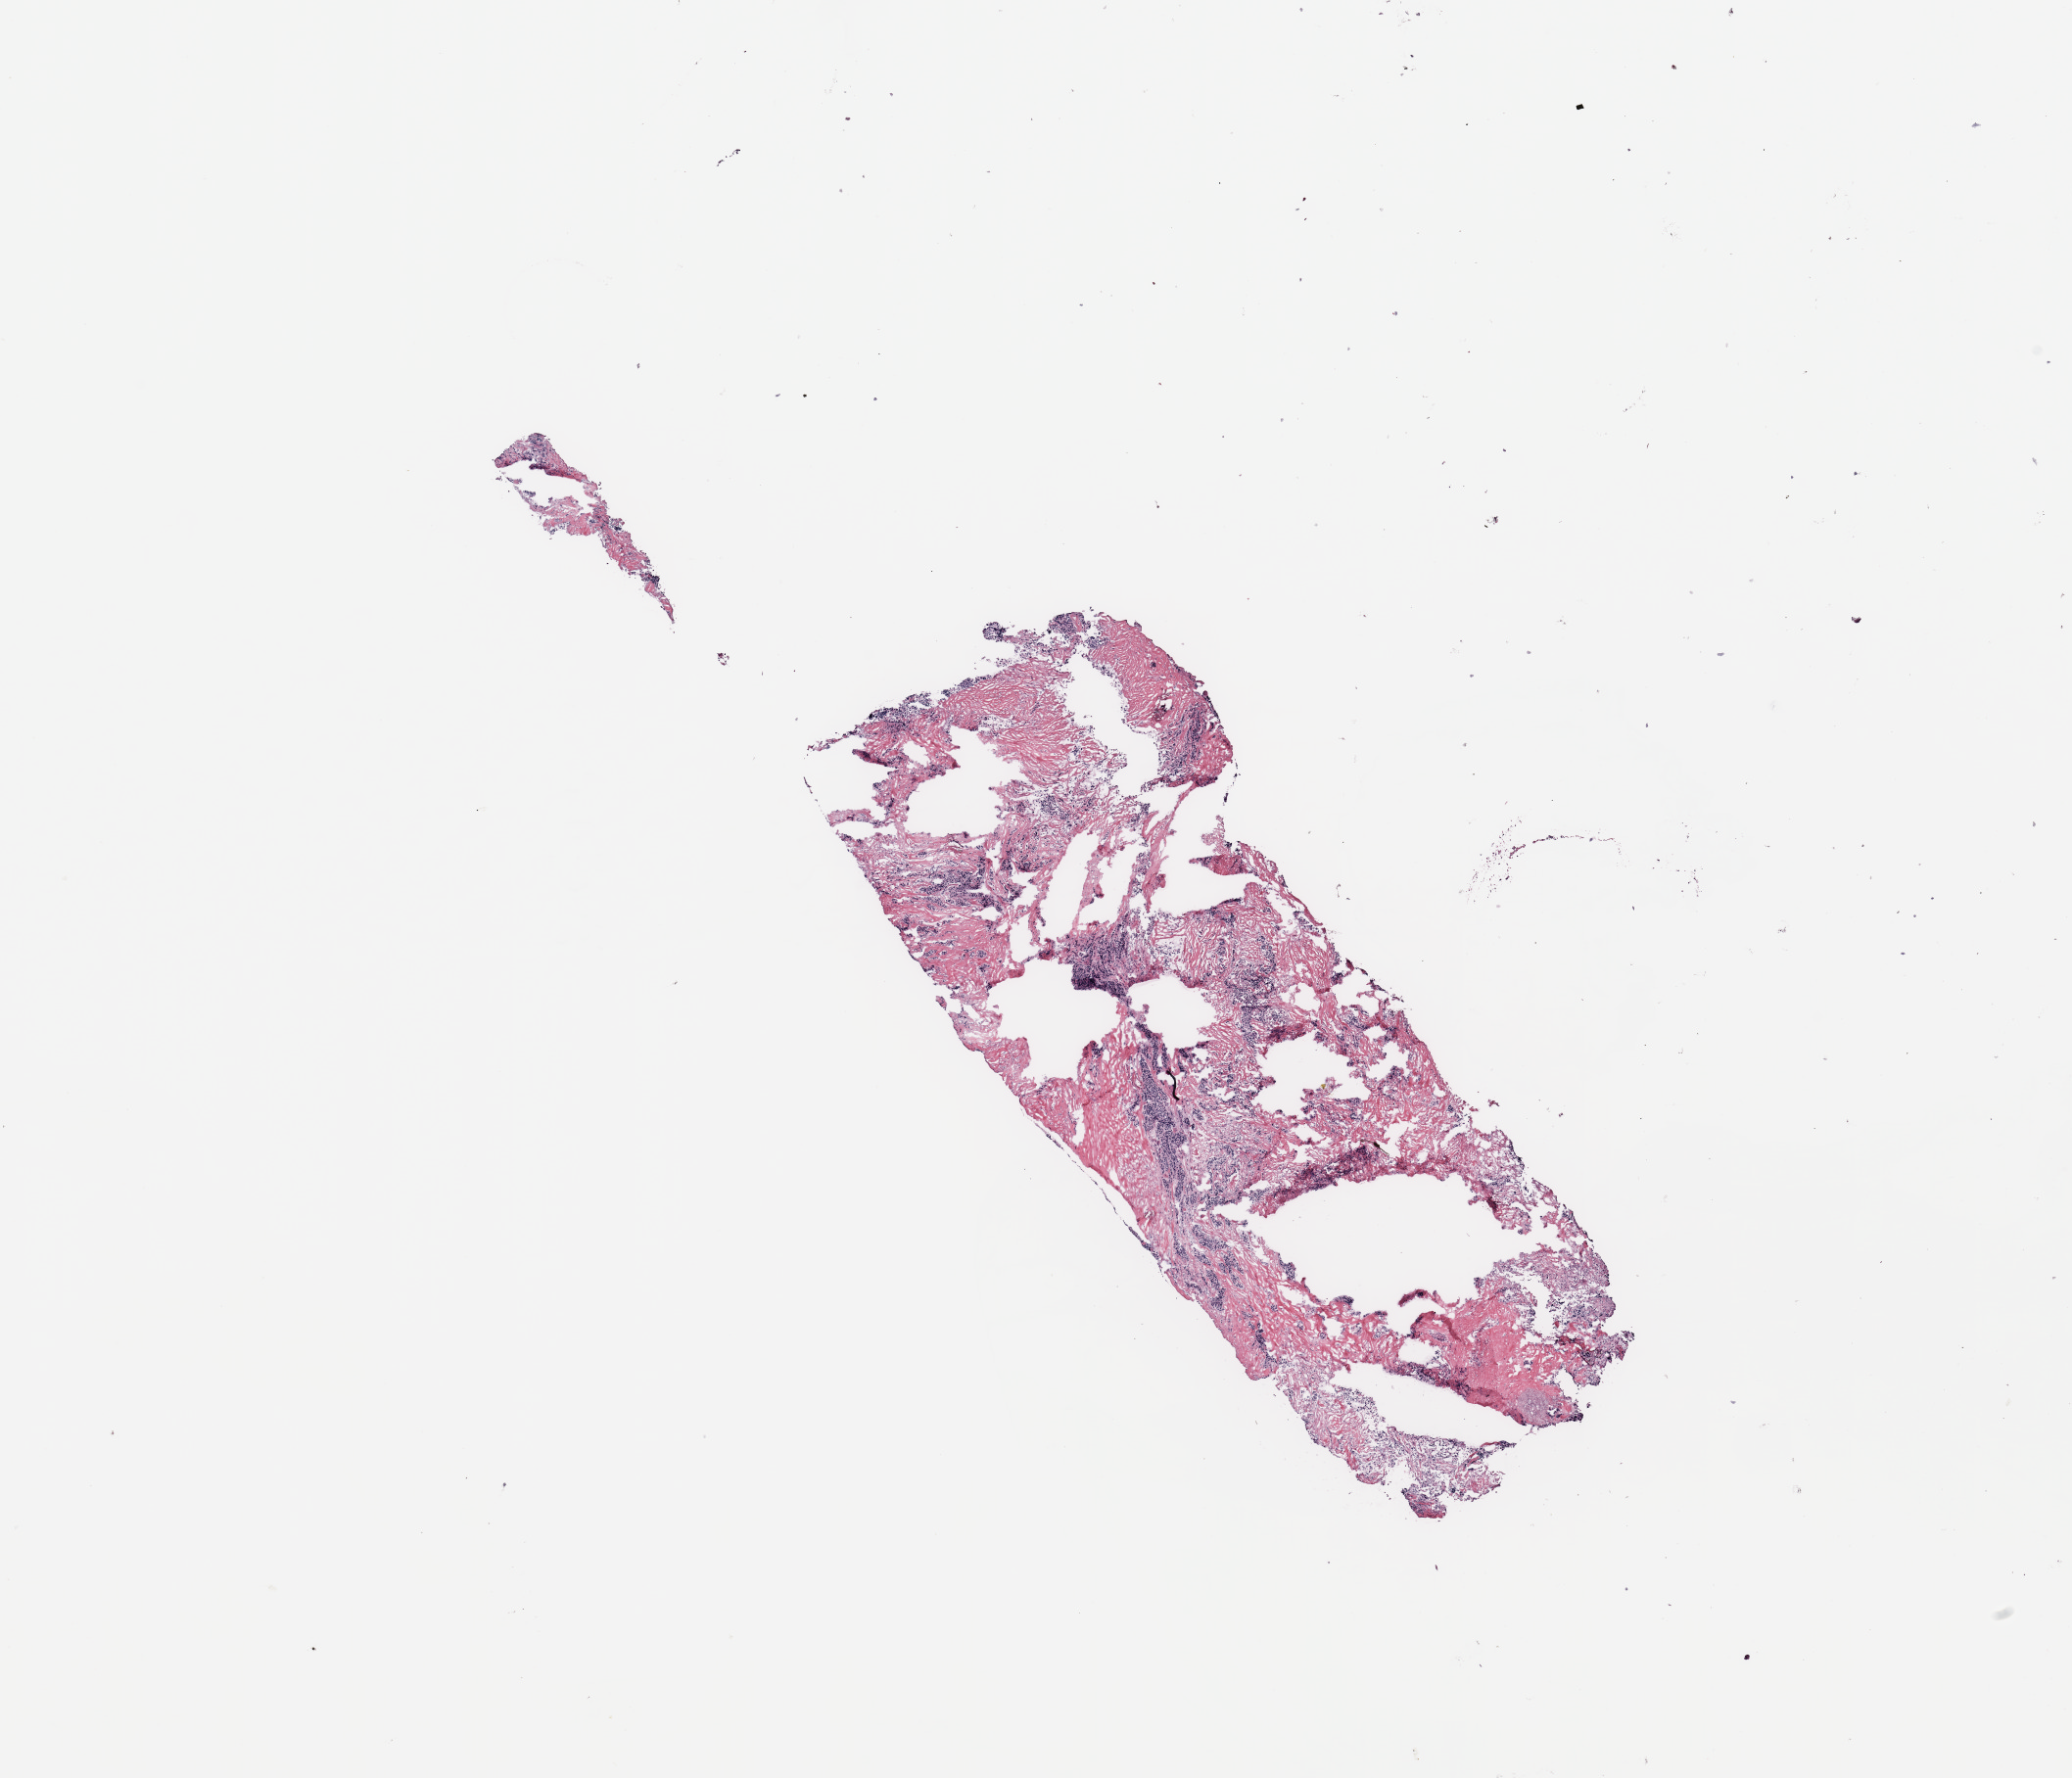
Digitized Hematoxylin and eosin (H&E) stained tissue section (whole slide) — a low-resolution overview of the entire scanned area, about 16.7 x 14.4 mm (from a 20x scan); breast, tumour tissue. 84-year-old female patient.
AJCC pathologic stage: IIIA. Histologic diagnosis: Infiltrating duct carcinoma, NOS.